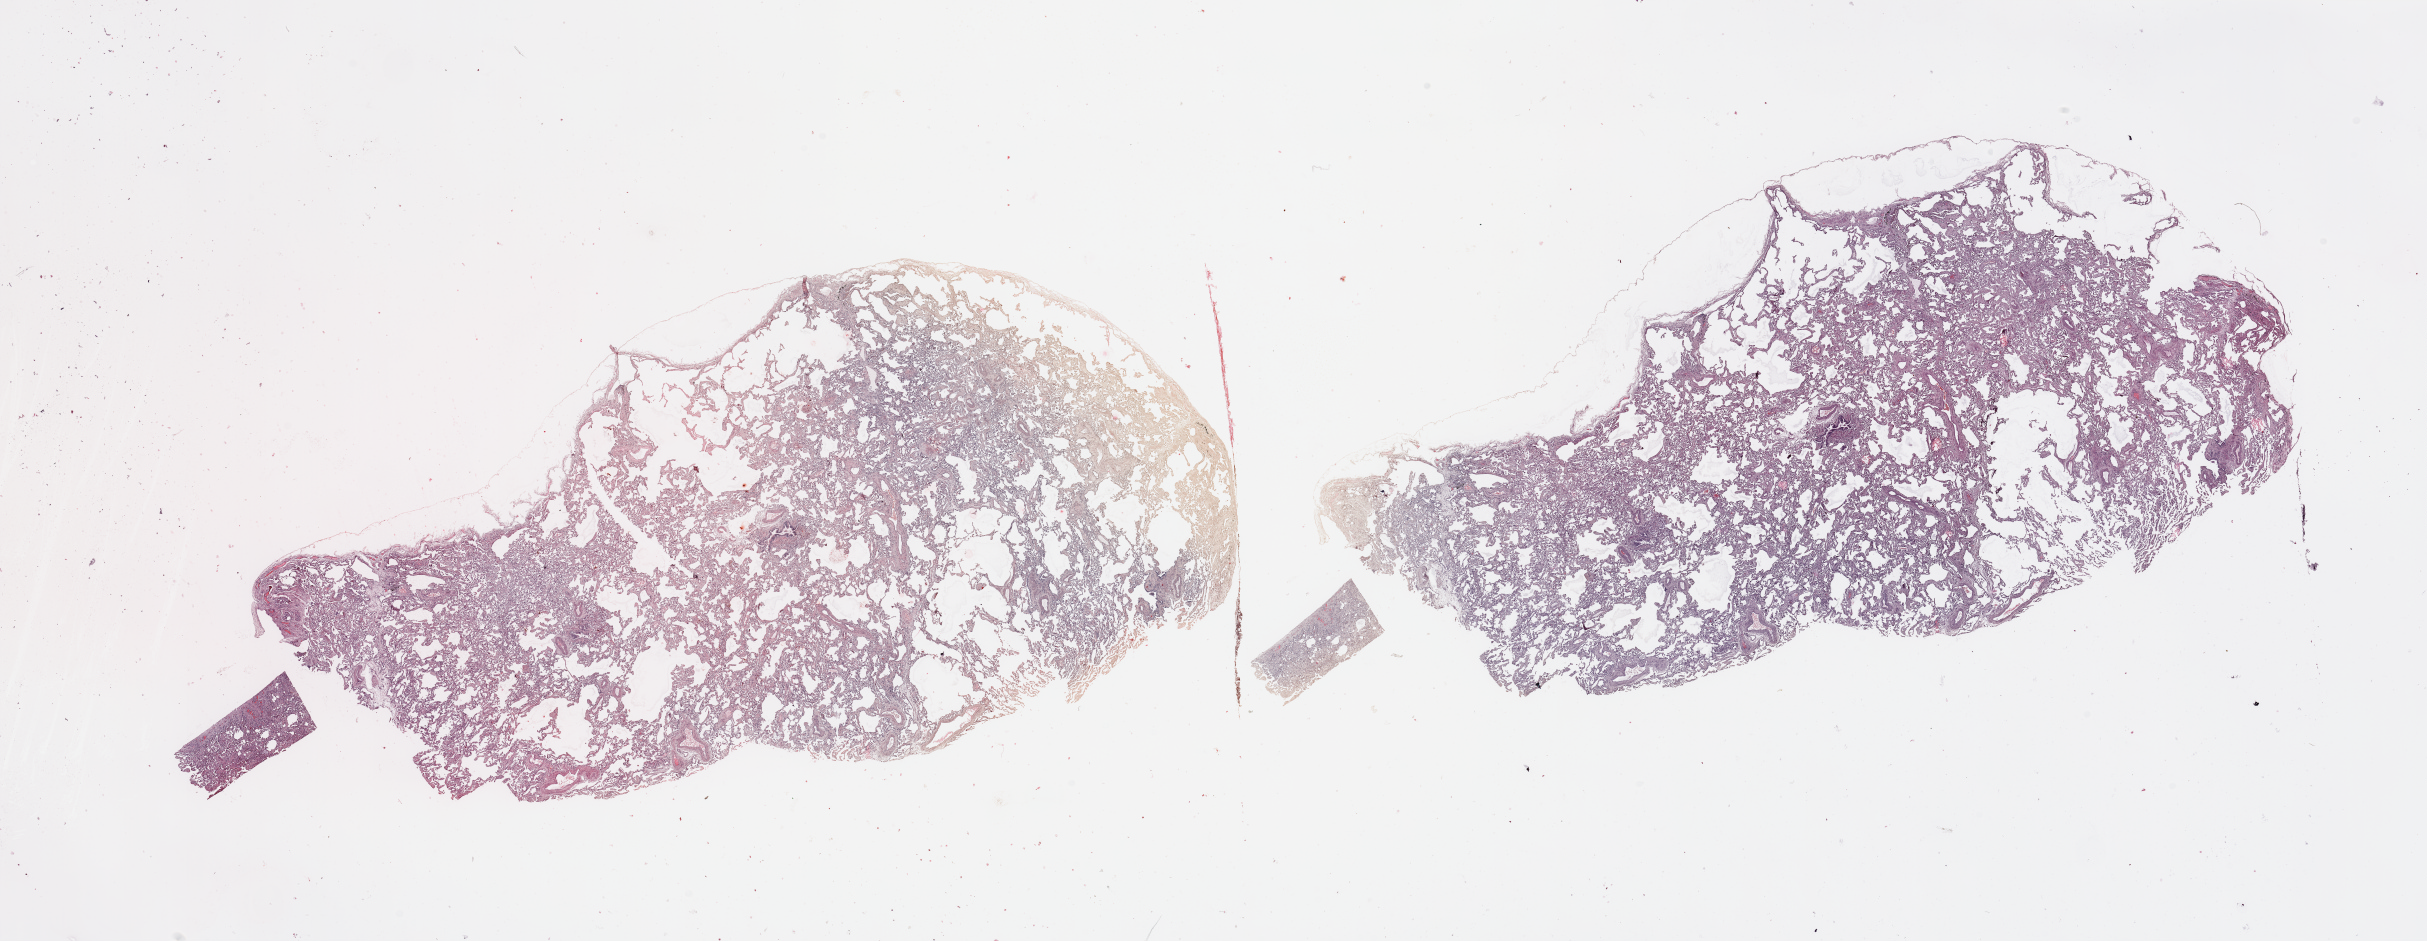
Whole-slide histology image, H&E, low-resolution overview of the scanned area, about 38.4 x 14.9 mm (from a 20x scan), normal (non-tumour) tissue sample, sampled site: lung. 64-year-old male patient.
• this section: normal (non-tumour) tissue from the same patient
• patient diagnosis: Adenocarcinoma, NOS